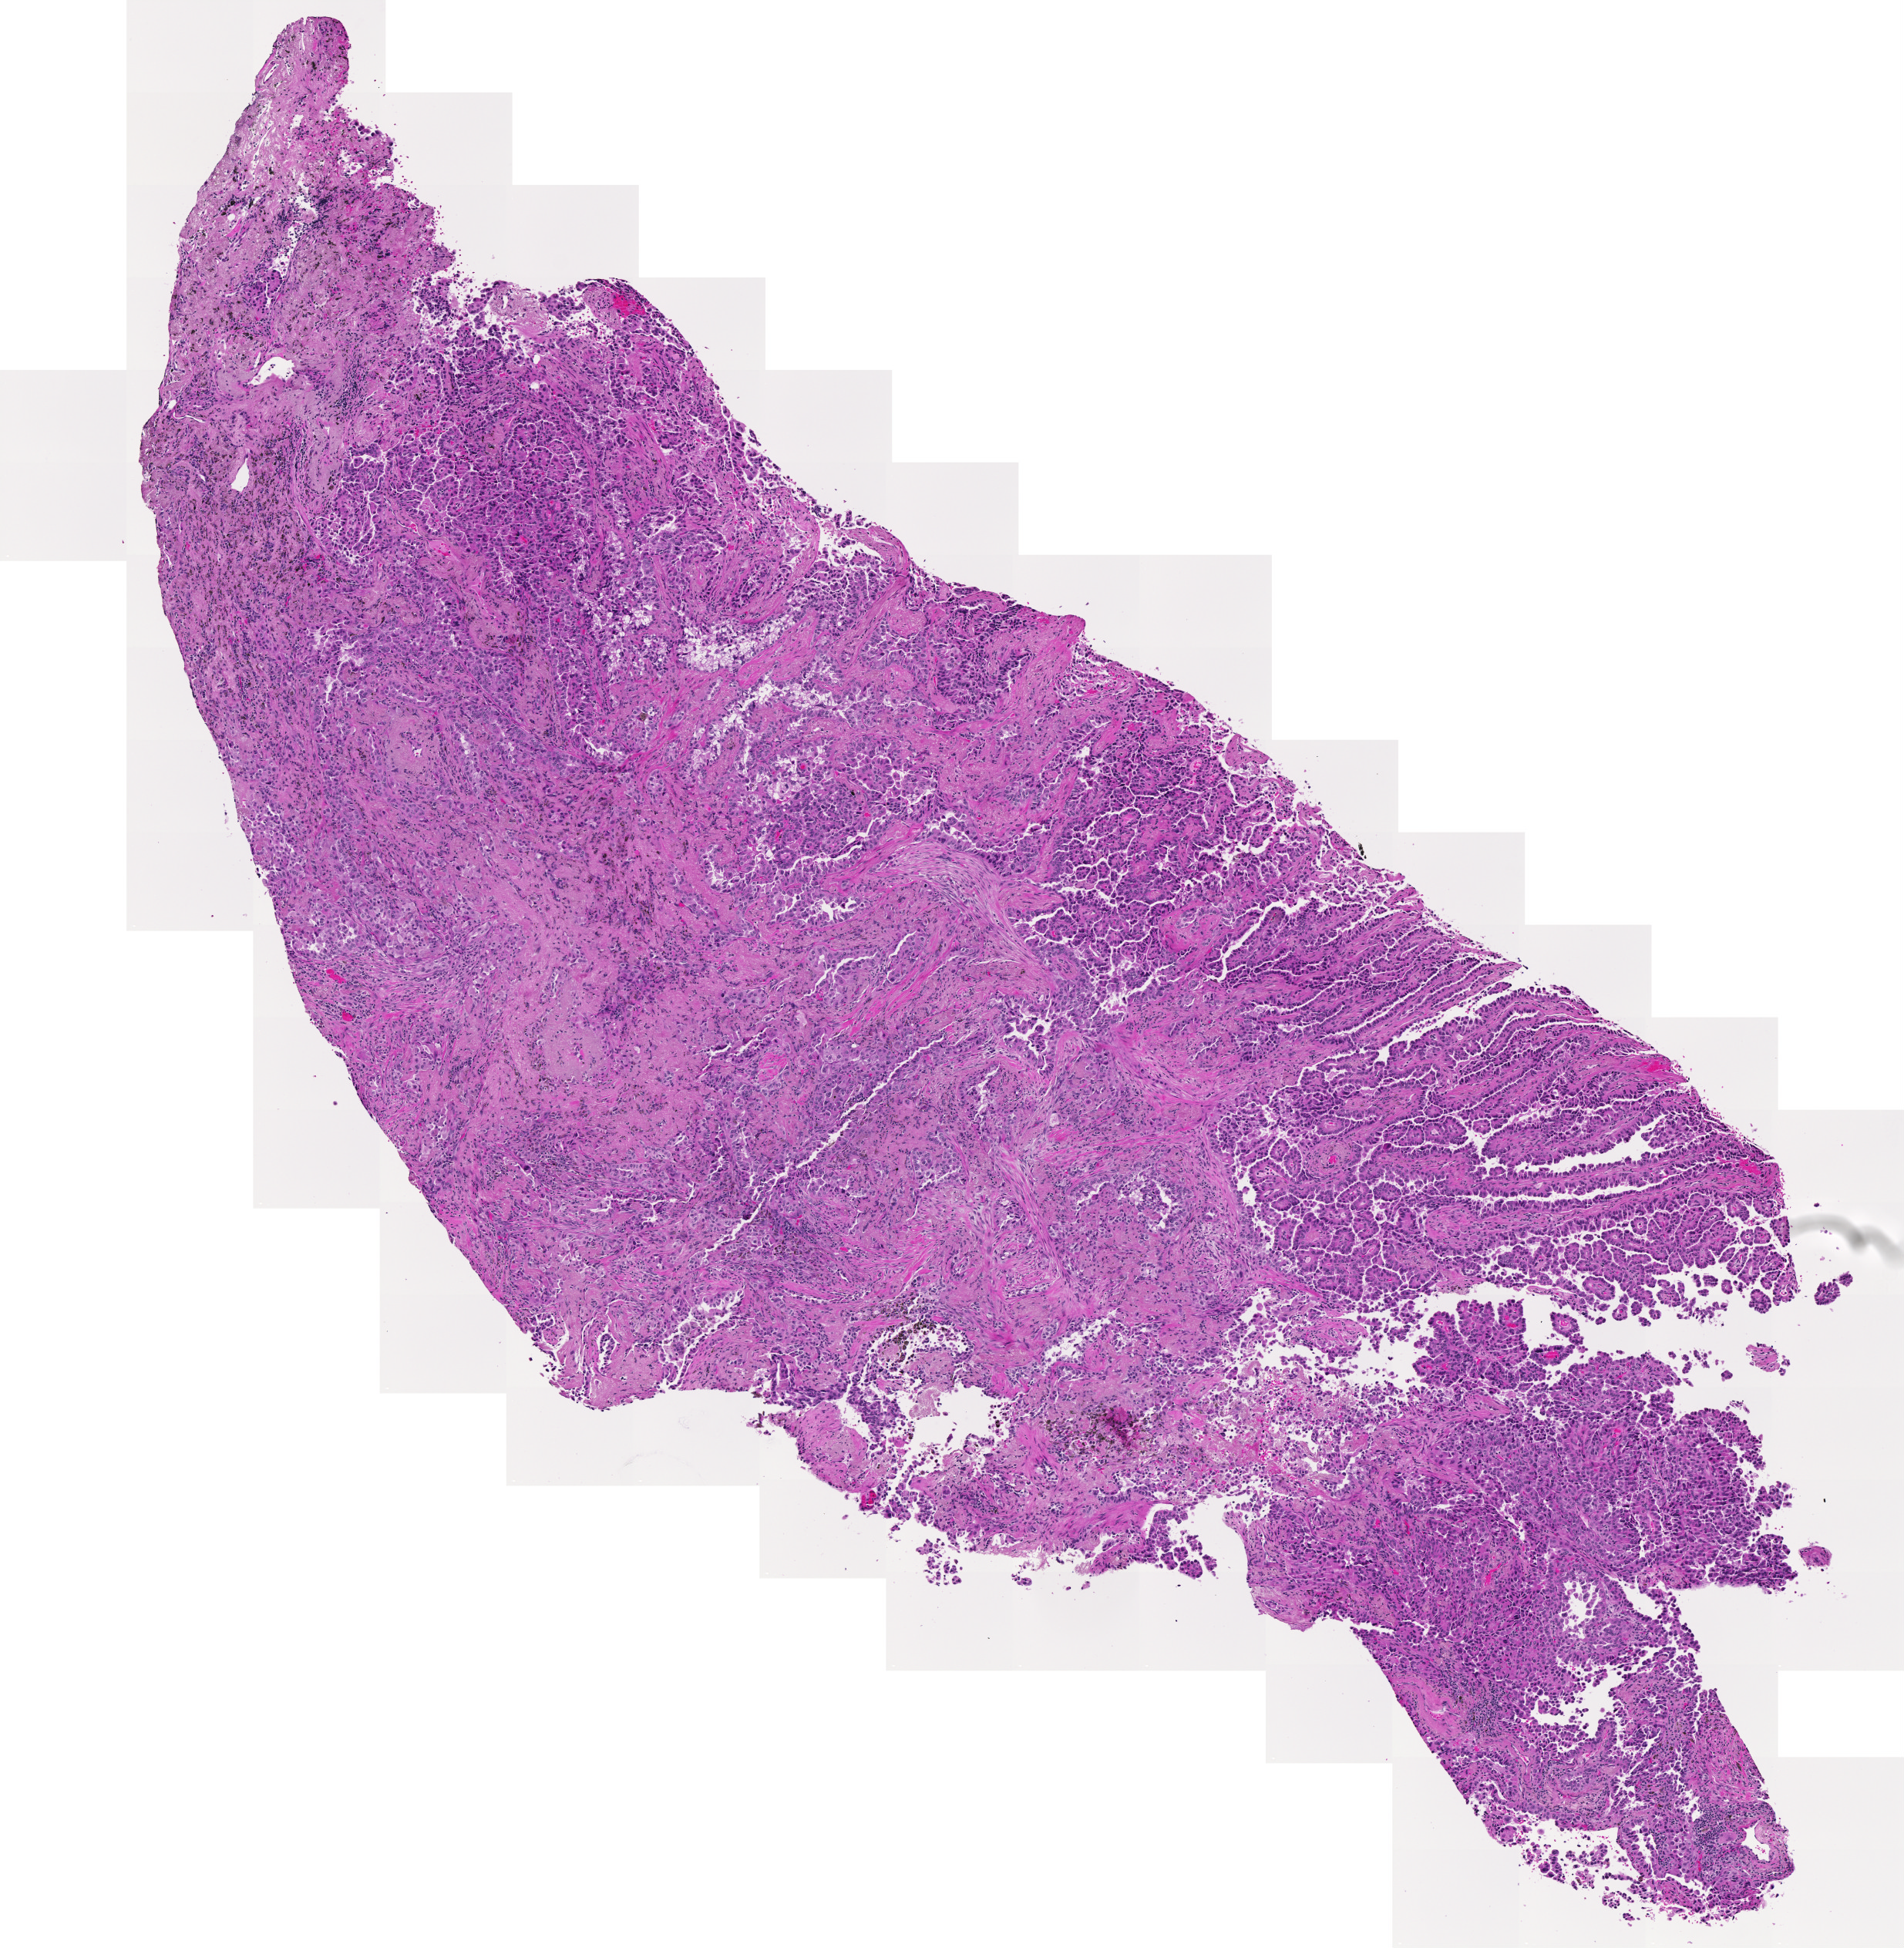
Whole-slide histology image, Hematoxylin and eosin (H&E) stained — whole scanned area (about 6.4 x 6.5 mm) shown as a low-resolution overview; tumour tissue sample, sampled site: lung. 64-year-old male patient. Histologic grade: G2 (moderately differentiated). Pathologist review of this section (percent, as recorded): tumour nuclei 70%, necrosis 5%.
Diagnosis: Adenocarcinoma, NOS. AJCC pathologic stage: IA3.